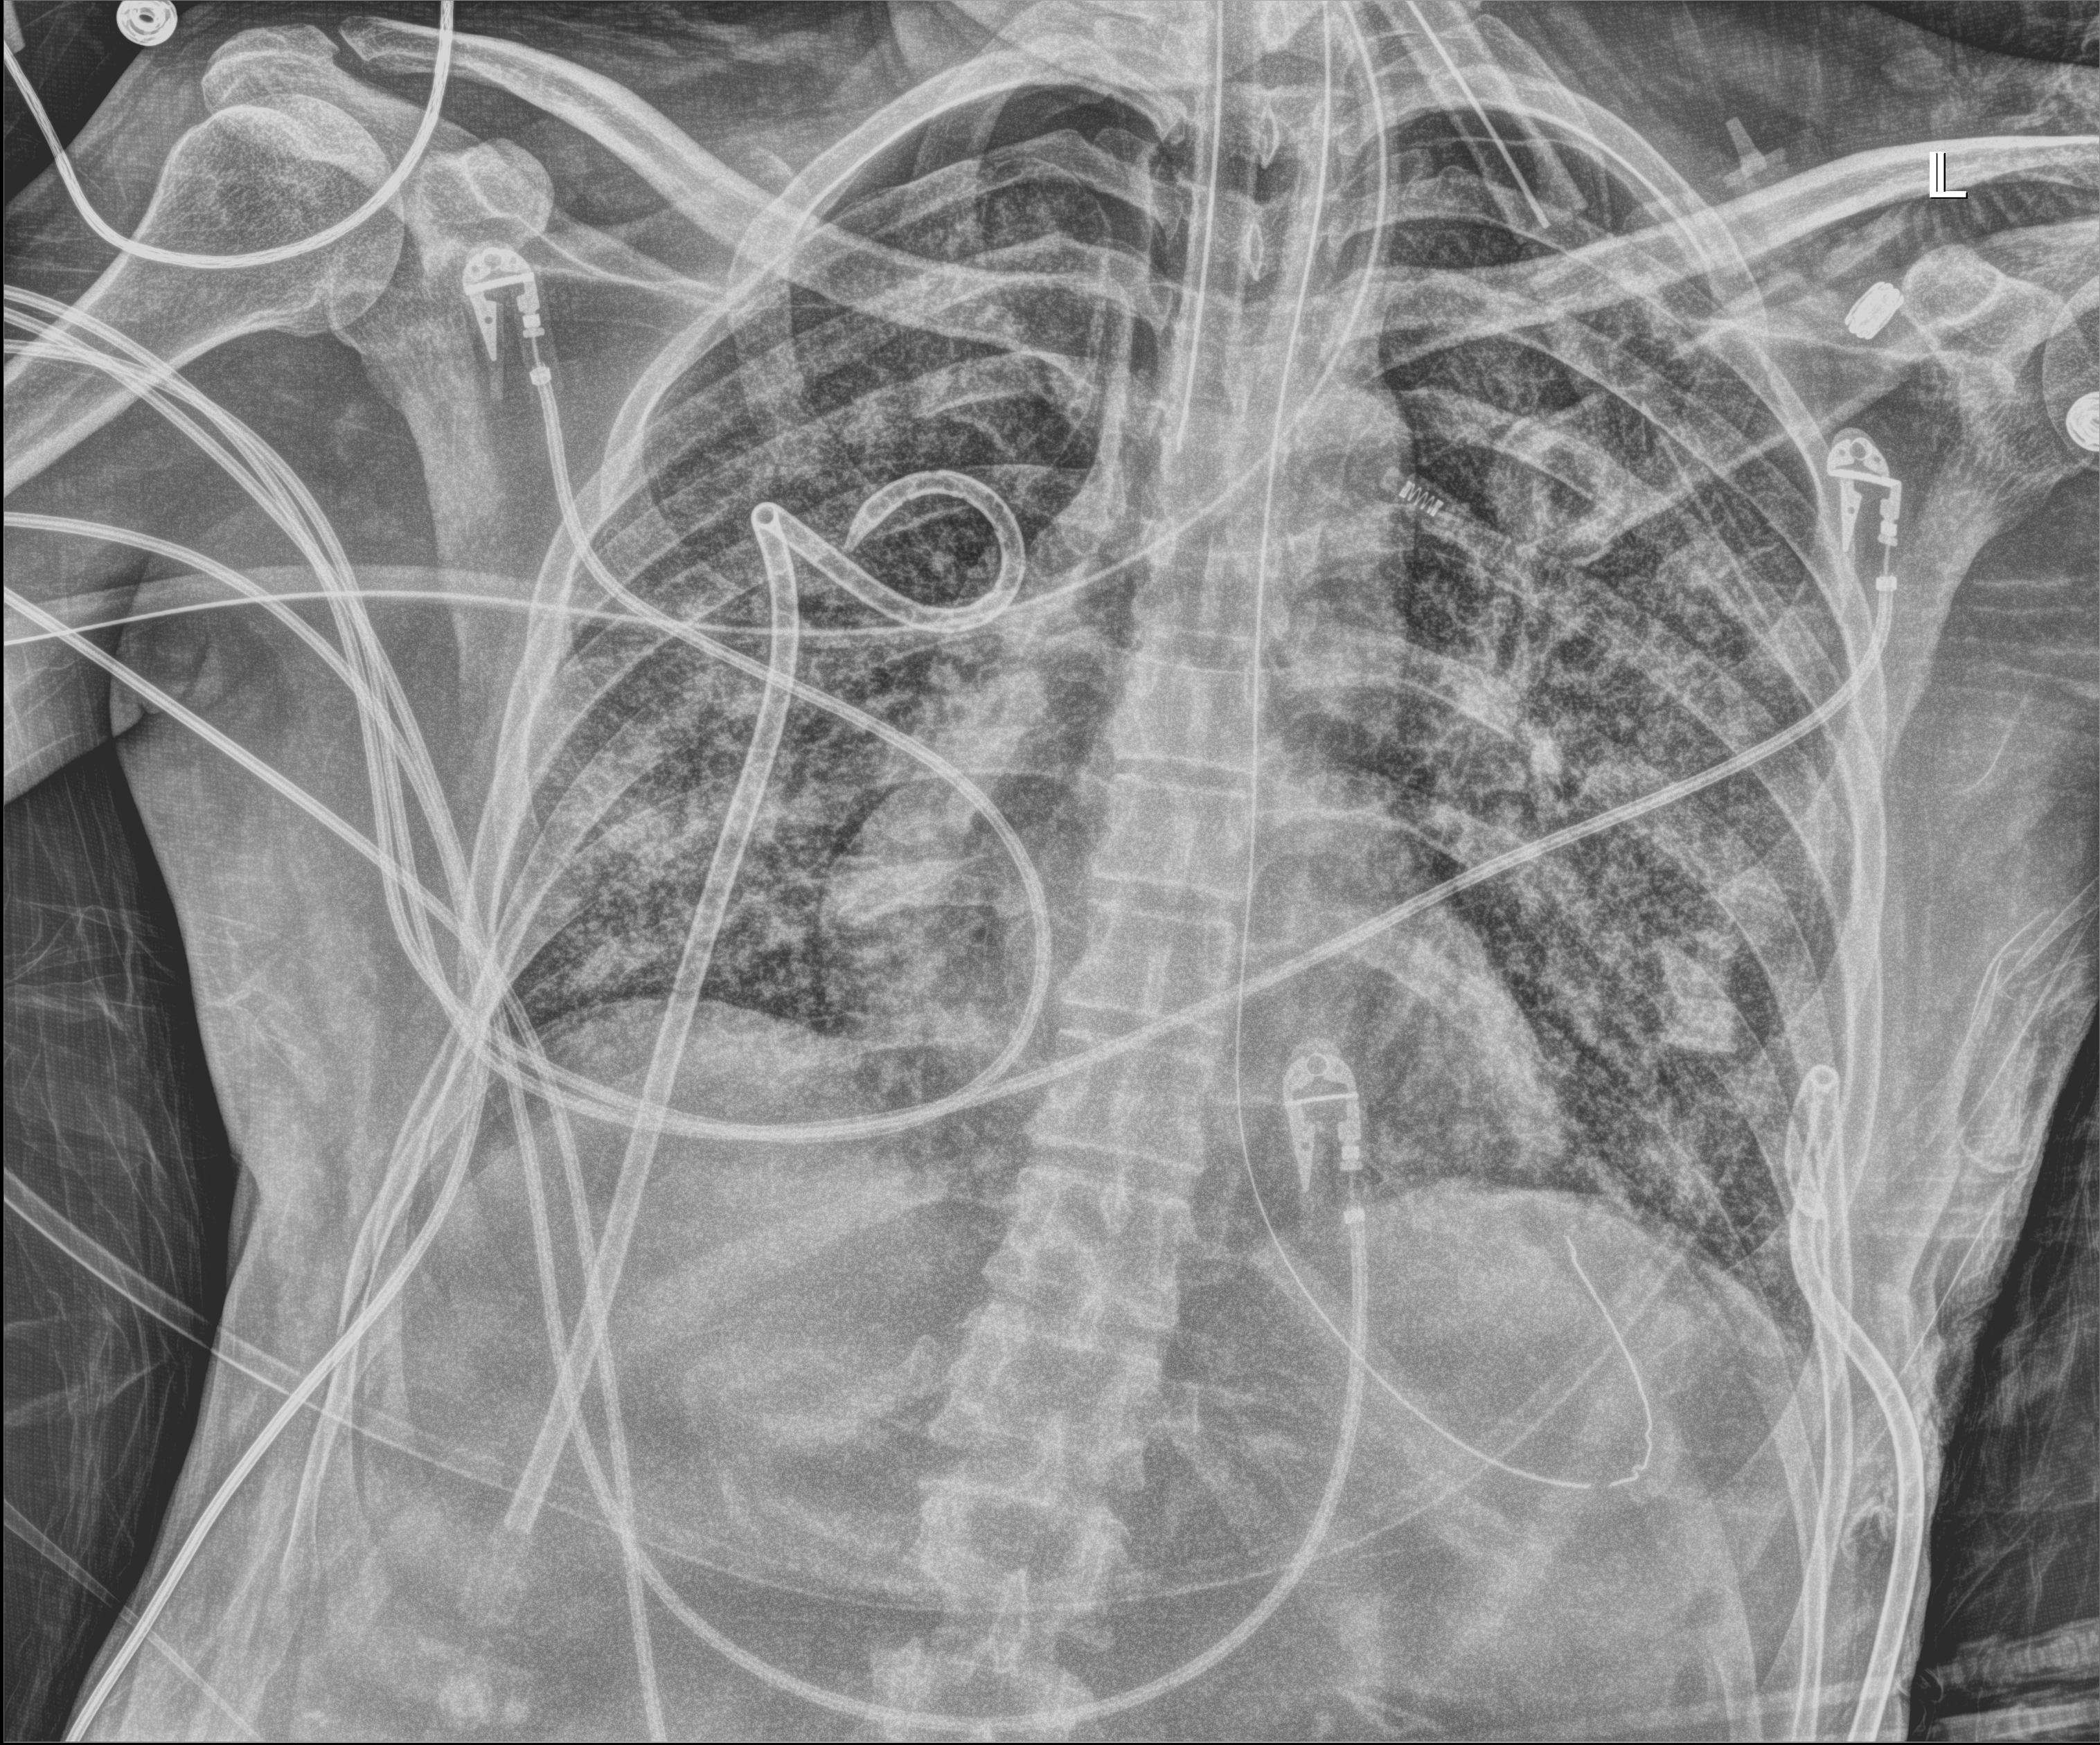
Chest X-ray (portable); anteroposterior (AP) projection. Patient hospitalised with COVID-19, aged 18–59 years.
From the hospital-stay record, not from the radiograph (when in the stay this image was taken is not recorded): mechanically ventilated during this hospital stay: yes; admitted to intensive care during this hospital stay: yes.